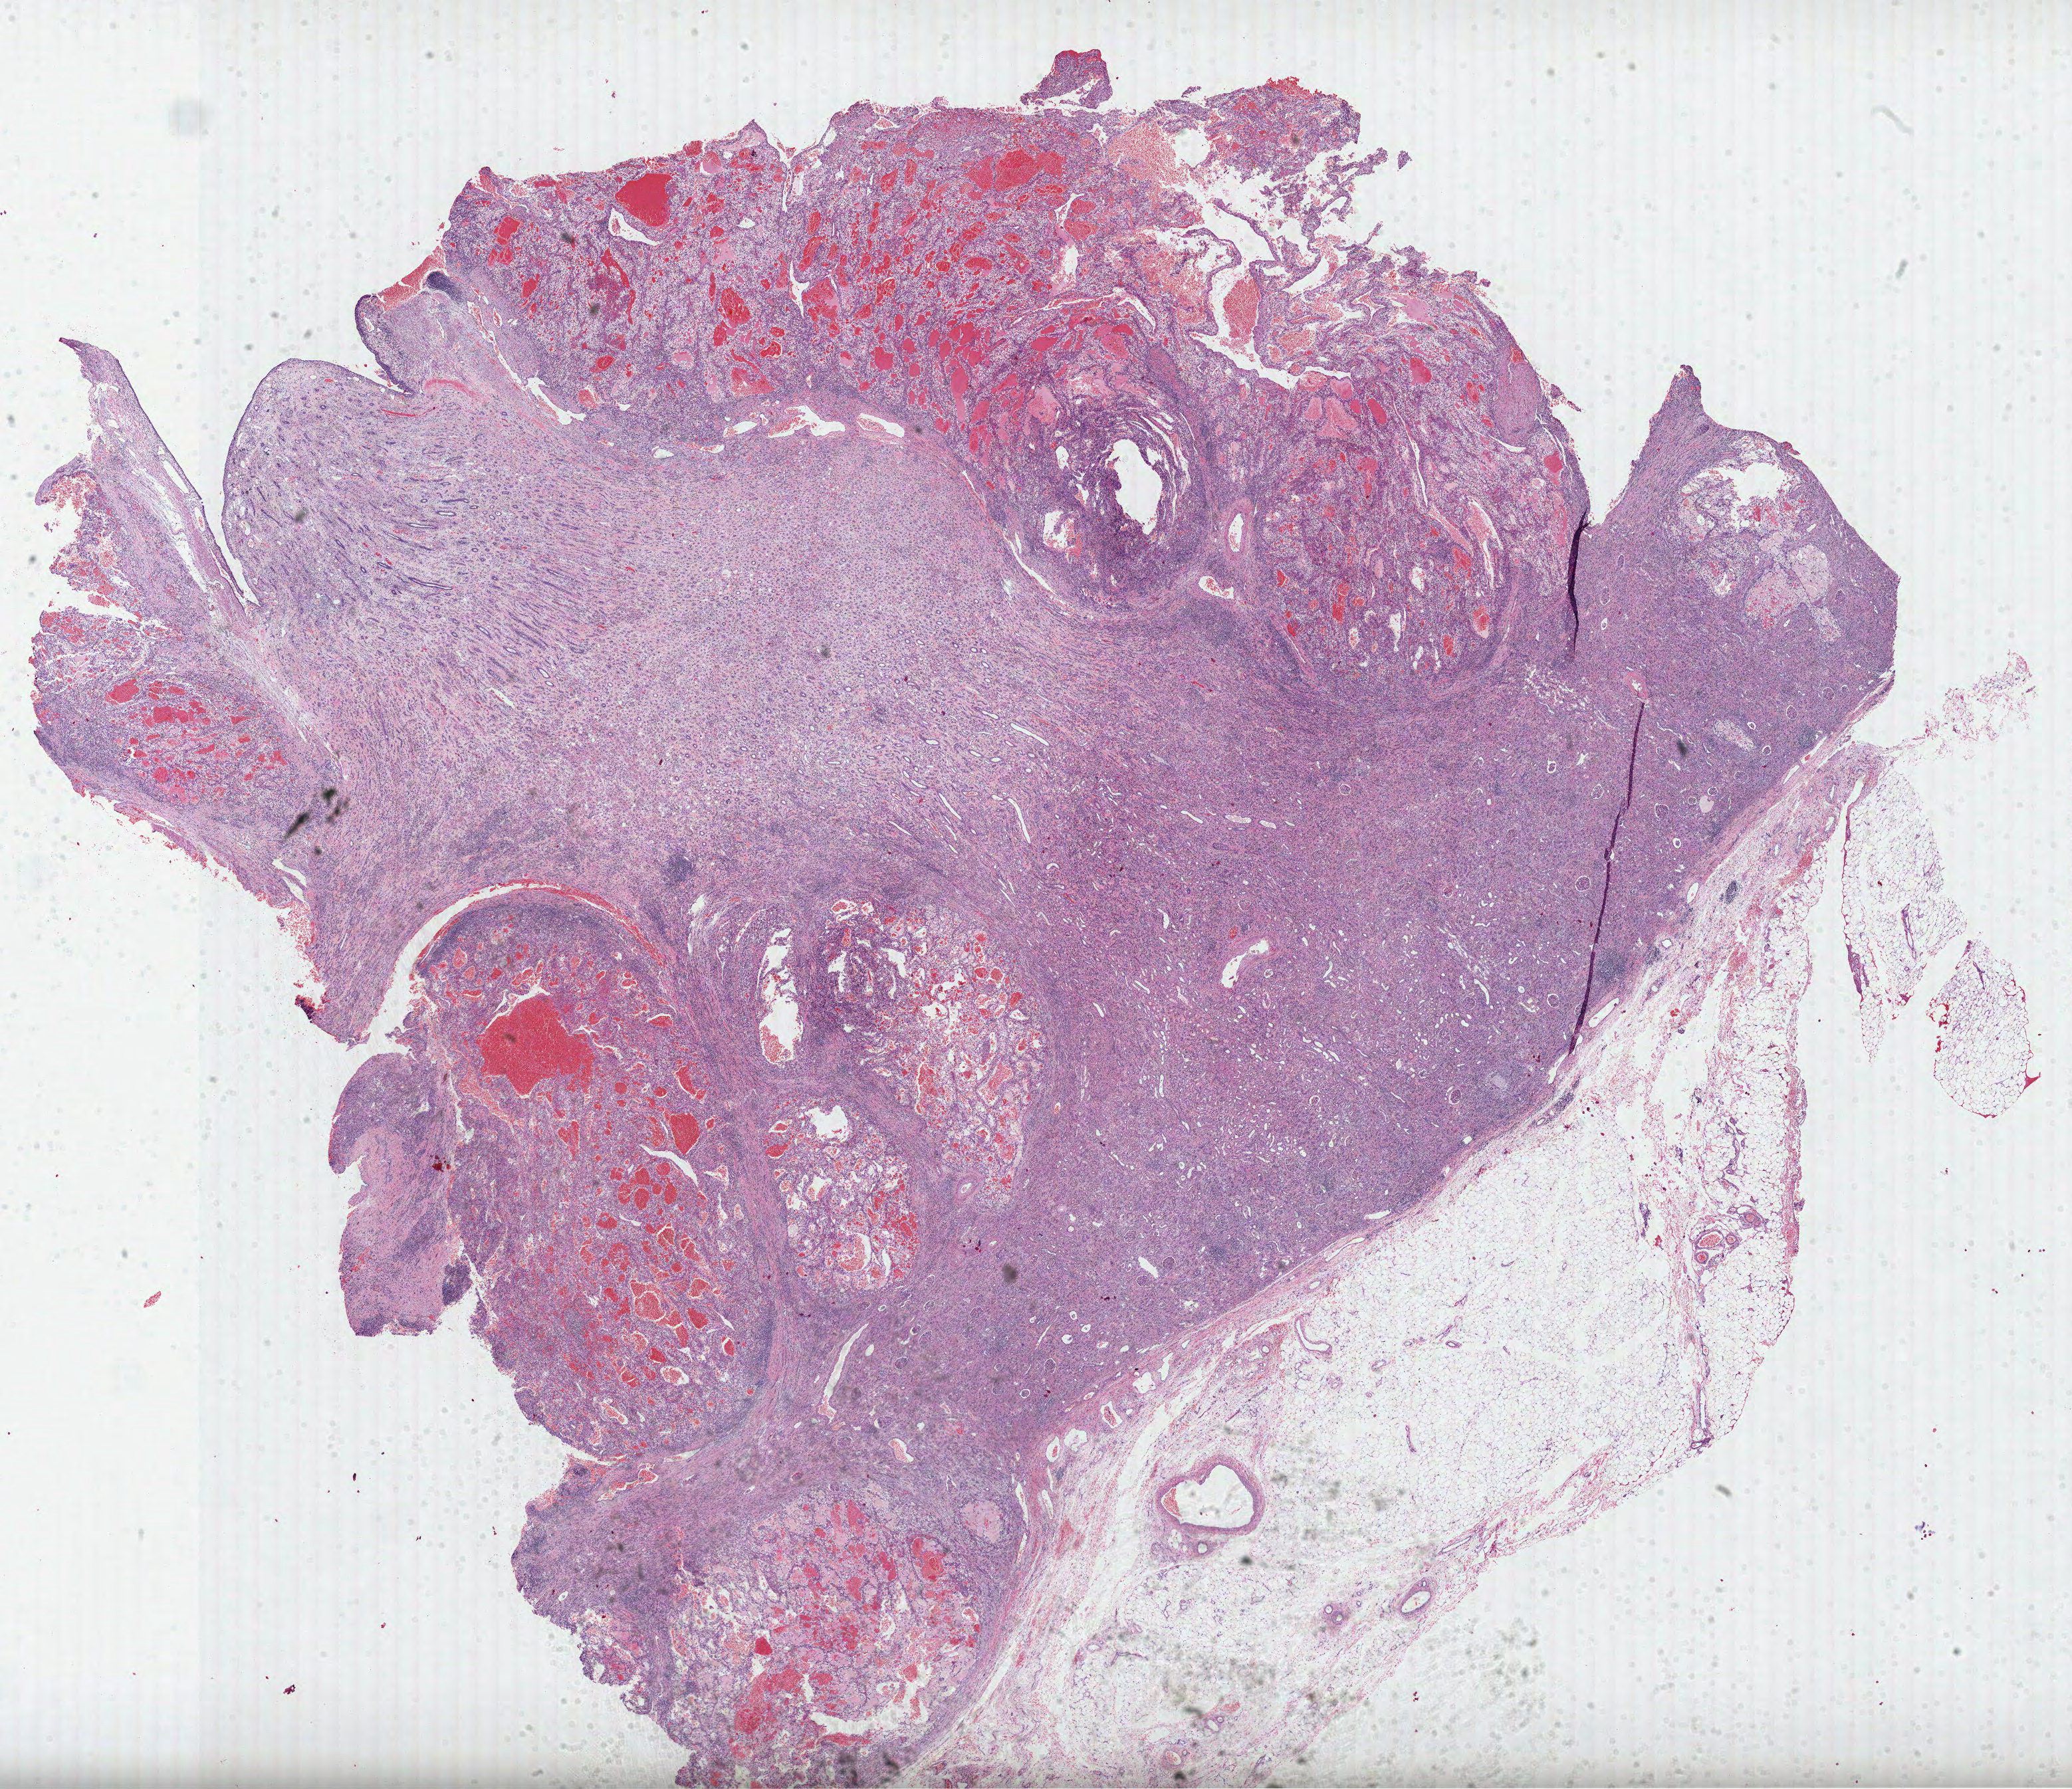
H&E-stained whole-slide image, a low-resolution overview of the entire scanned area, about 25.1 x 21.7 mm, formalin-fixed paraffin-embedded (FFPE) diagnostic section, kidney, primary tumour sample. Male patient; age at initial diagnosis 52 years. Histologic grade: G3 (poorly differentiated).
Laterality: right. Diagnosis: Clear cell adenocarcinoma, NOS. AJCC pathologic stage: III (7th edition). TNM: T3b N0 M0.